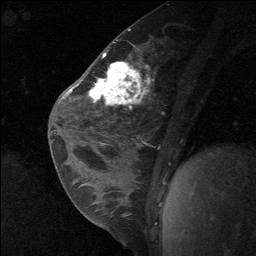
Breast MRI (dynamic contrast-enhanced), one sagittal slice. Slice 33 of 64 in the series (ordered by position). Dynamic contrast-enhanced study with each time point stored as its own series, time point 2 of 3 at this slice position (early post-contrast, ordered by acquisition time). 1.5 T. TE 4.8 ms, TR 27 ms. 256 × 256 image matrix. Female patient, age 26 years. From the clinical record (not read from this slice): setting: breast cancer imaged before/during neoadjuvant chemotherapy; receptor status: HR-positive, HER2-negative.
Outlined on this slice (semi-automatically segmented with operator editing):
- analysis volume of interest (the breast-tissue region the enhancement analysis was run in; not a lesion): bounding box [x1, y1, x2, y2] px = [86, 43, 135, 138]
- tumour enhancement mask (voxels above the 90 % enhancement threshold inside the analysis volume of interest): [89, 63, 126, 102]